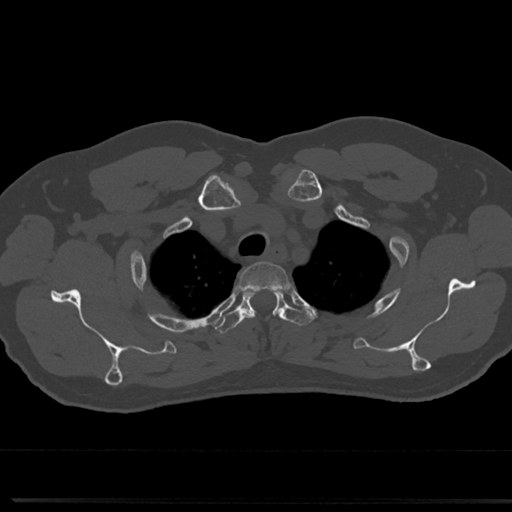
CT including the spine, one axial slice; position 608 of 817 along the scan axis; reconstruction kernel Br40s/3; bone window (W 1800 / L 400 HU); 0.5 mm slice thickness; 512 × 512 image matrix. Patient: male, 61 years. From the clinical record (not read from this slice): primary cancer: prostate.
Annotated regions visible in this slice (semi-automatically segmented with operator editing):
- T2 vertebra: bounding box <239,262,288,285> (left, top, right, bottom; pixels)
- T3 vertebra: <215,286,305,333>